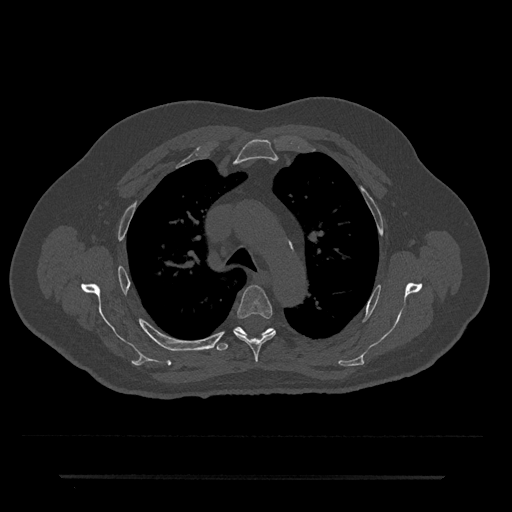
CT including the spine, one axial slice; 120 kVp; bone window (W 1800 / L 400 HU); 0.5 mm slice thickness; 512 × 512 image matrix. Patient: male, 69 years. Case-level facts recorded for this patient, not image findings: primary cancer: prostate.
Structures marked on this image (semi-automatically segmented with operator editing):
- T4 vertebra: bounding box <234,285,276,362> (left, top, right, bottom; pixels)
- T5 vertebra: <215,327,274,351>